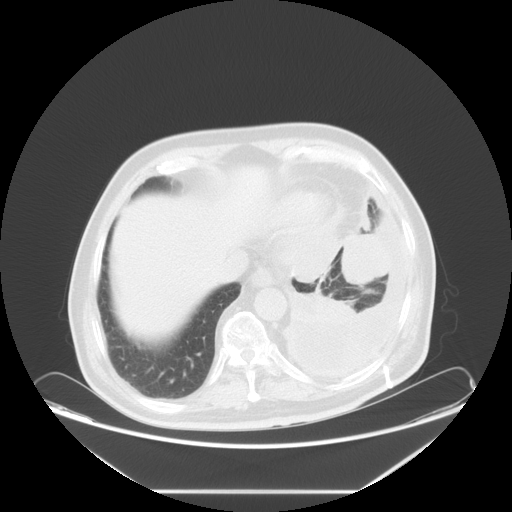
Chest CT, one axial slice. Slice 17 of 63 in the series (ordered by position). Reconstruction kernel STANDARD. 120 kVp. Lung window (W 1500 / L -600 HU). 5 mm slice thickness. 512 × 512 image matrix, field of view 448 × 448 mm. Male patient, age 67 years. From the clinical record (not read from this slice): clinical TNM (as recorded): T1b N1 M1a; histopathological grade: G3.
Structures marked on this image (bounding box drawn by a radiologist):
- lung tumour (recorded histology: small cell carcinoma): bounding box <338,225,393,288> (left, top, right, bottom; pixels)